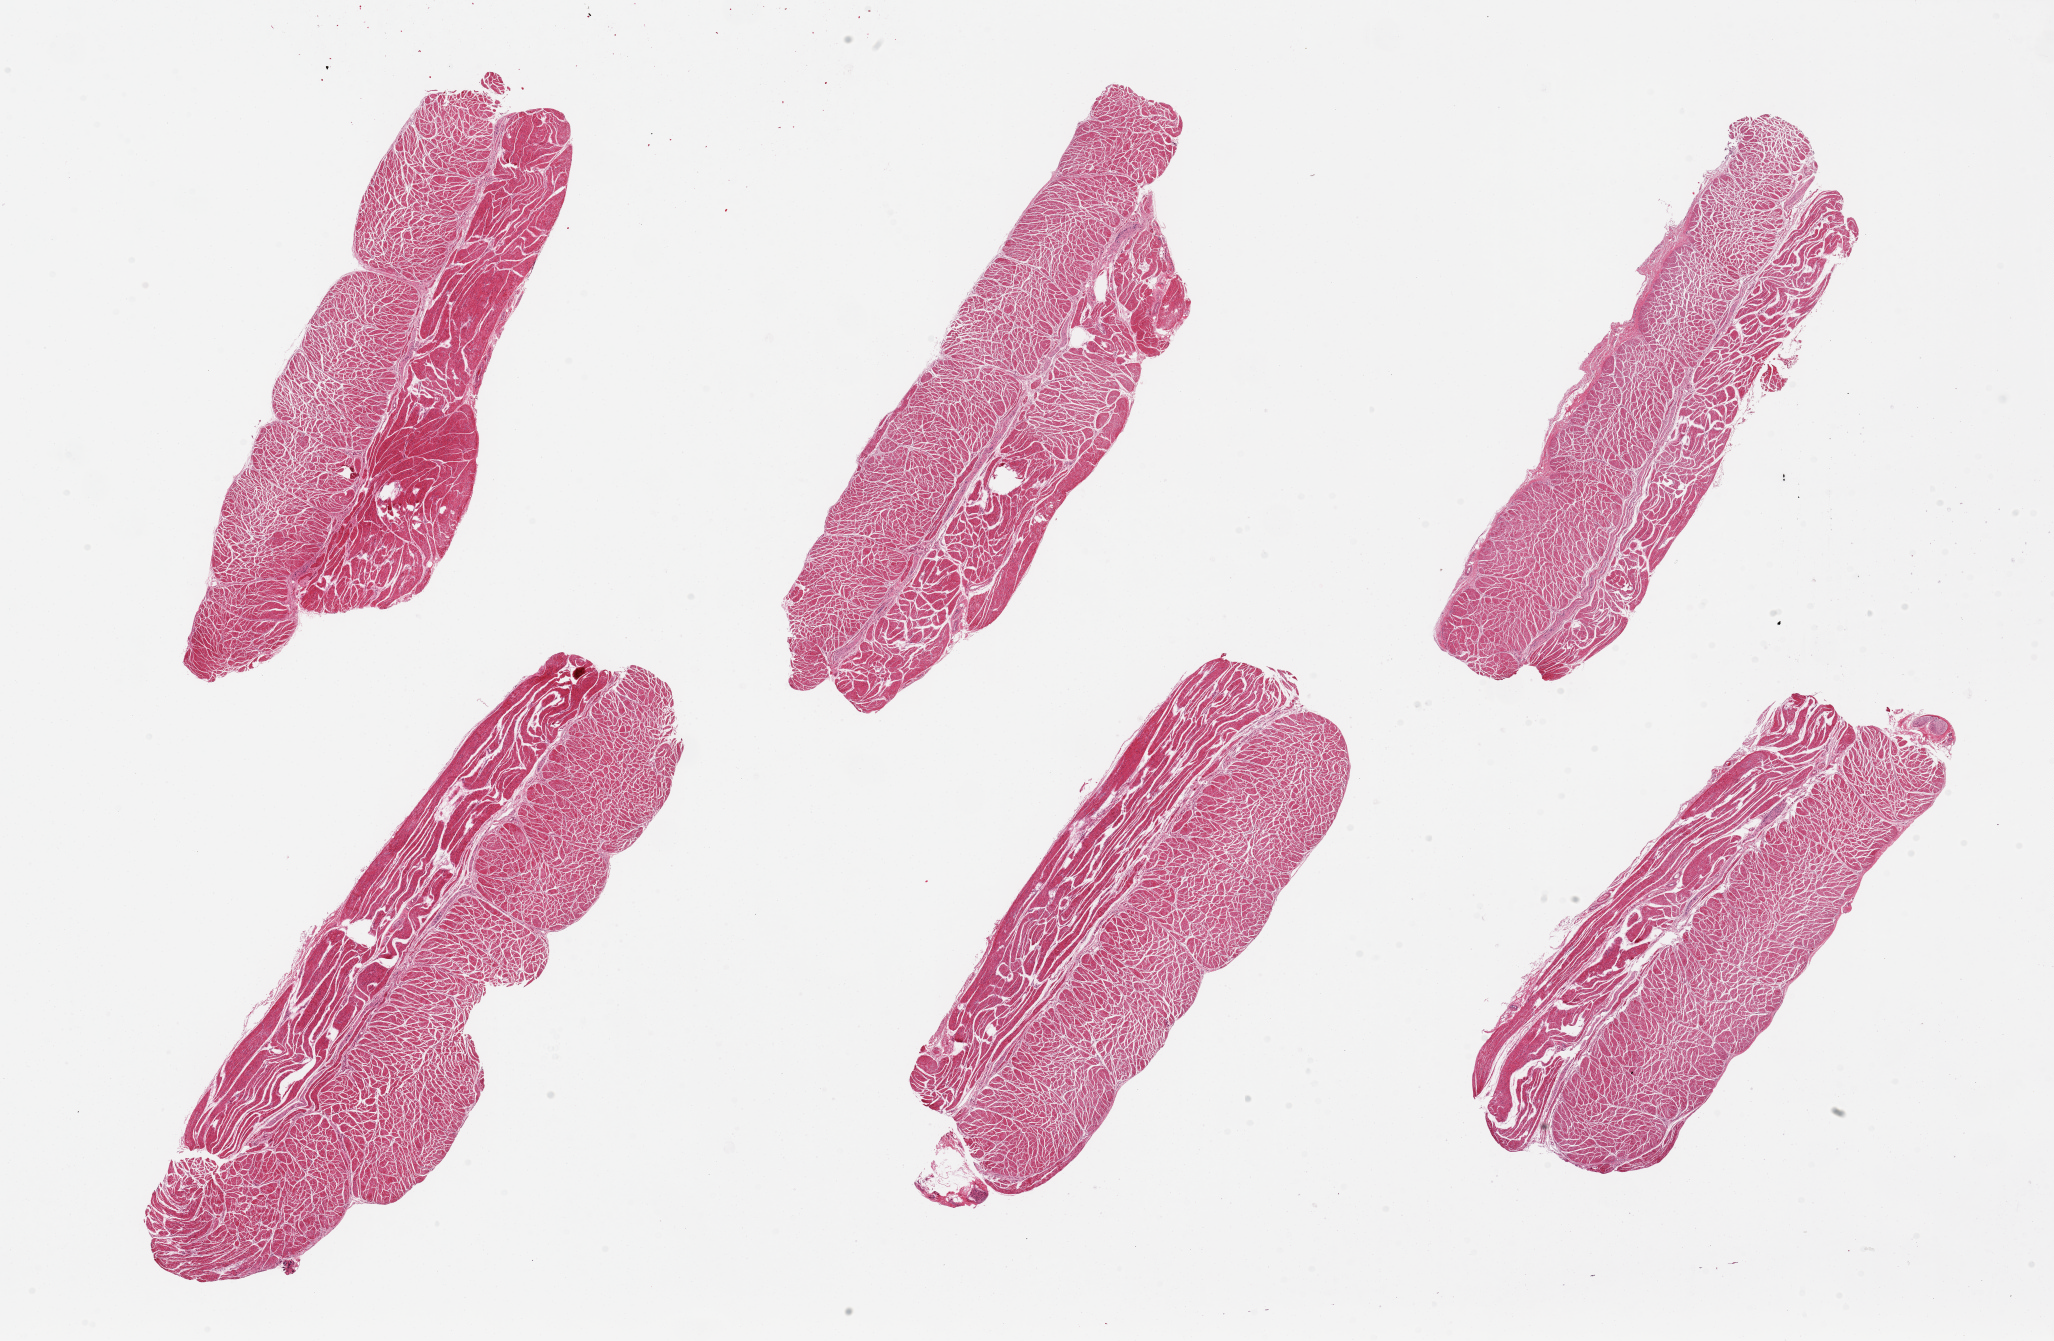
Whole-slide image, hematoxylin and eosin (H&E) stain — shown as a low-resolution overview of the whole scanned area (about 32.5 x 21.2 mm, acquisition: 20x scan); PAXgene-fixed paraffin-embedded (PFPE) section; sampled site (target tissue): esophageal muscle; donor tissue sample. Donor: female.
Pathologist's review note for this sample: 6 pieces, up to 12x4mm; all muscle; good specimens.